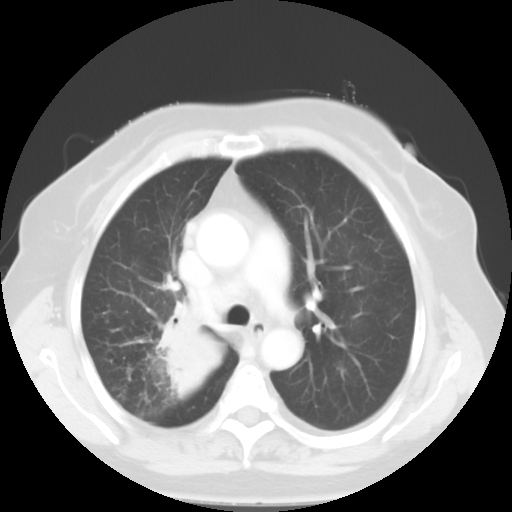
Chest CT, one axial slice. Position 35 of 52 along the scan axis. Reconstruction kernel STANDARD. 120 kVp. Lung window (W 1500 / L -600 HU). 512 × 512 image matrix. Patient: female, 81 years. From the clinical record (not read from this slice): clinical TNM (as recorded): T4 N3 M1b.
Annotated regions visible in this slice (bounding box drawn by a radiologist):
- lung tumour (recorded histology: adenocarcinoma): box from (x=150, y=306) to (x=223, y=396) px